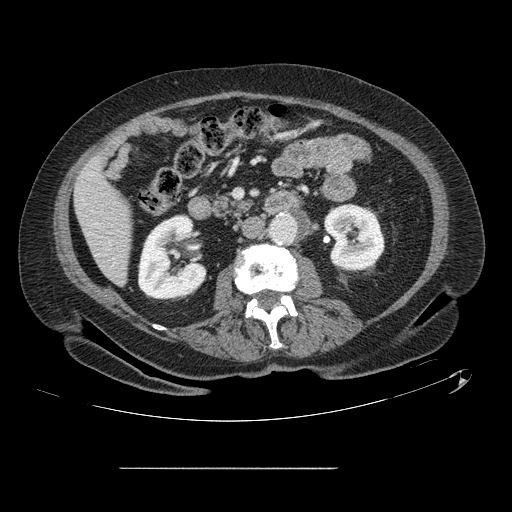
Contrast-enhanced abdominal CT, one axial slice; intravenous contrast given; soft-tissue window (W 400 / L 40 HU); 2.5 mm slice thickness; 512 × 512 image matrix, field of view 439 × 439 mm. Female patient, age 75 years. Case-level facts recorded for this patient, not image findings: diagnosis: colorectal cancer liver metastases, imaged before liver resection; multiple liver metastases: no; largest metastasis: 2.4 cm; chemotherapy before resection: no.
Structures marked on this image (outlined manually by an expert reader):
- liver: bounding box <75,159,131,284> (left, top, right, bottom; pixels)
- planned liver remnant (the part of the liver to remain after resection): <75,159,131,284>